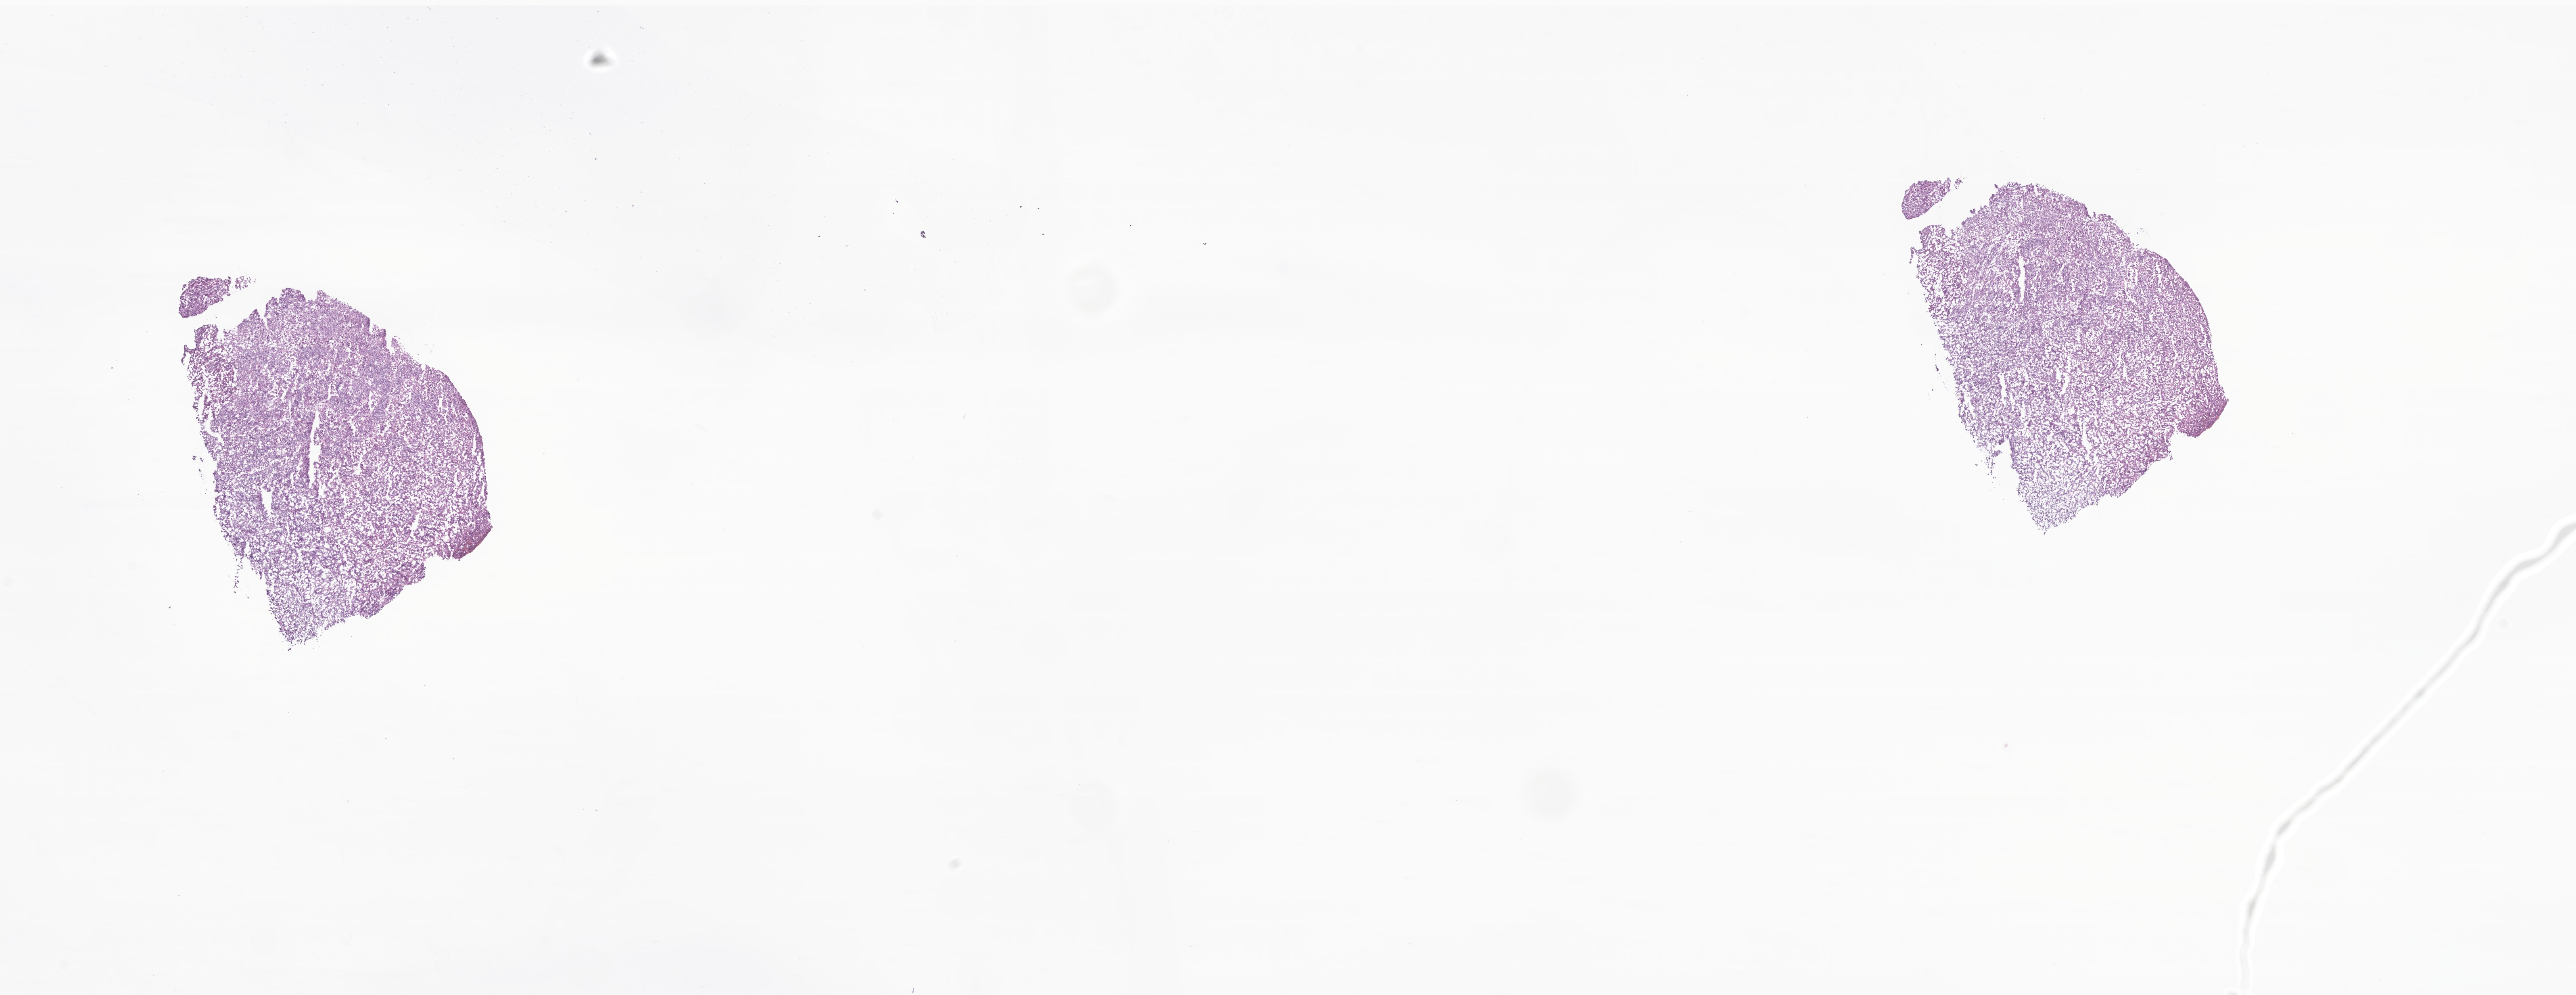
Hematoxylin and eosin (H&E) whole-slide image of tumor tissue from the pineal gland, whole scanned area (about 26.9 x 10.4 mm) shown as a low-resolution overview. Frozen section (OCT-embedded). Male patient, age 197 months.
Recorded diagnosis: Neoplasm, uncertain whether benign or malignant.